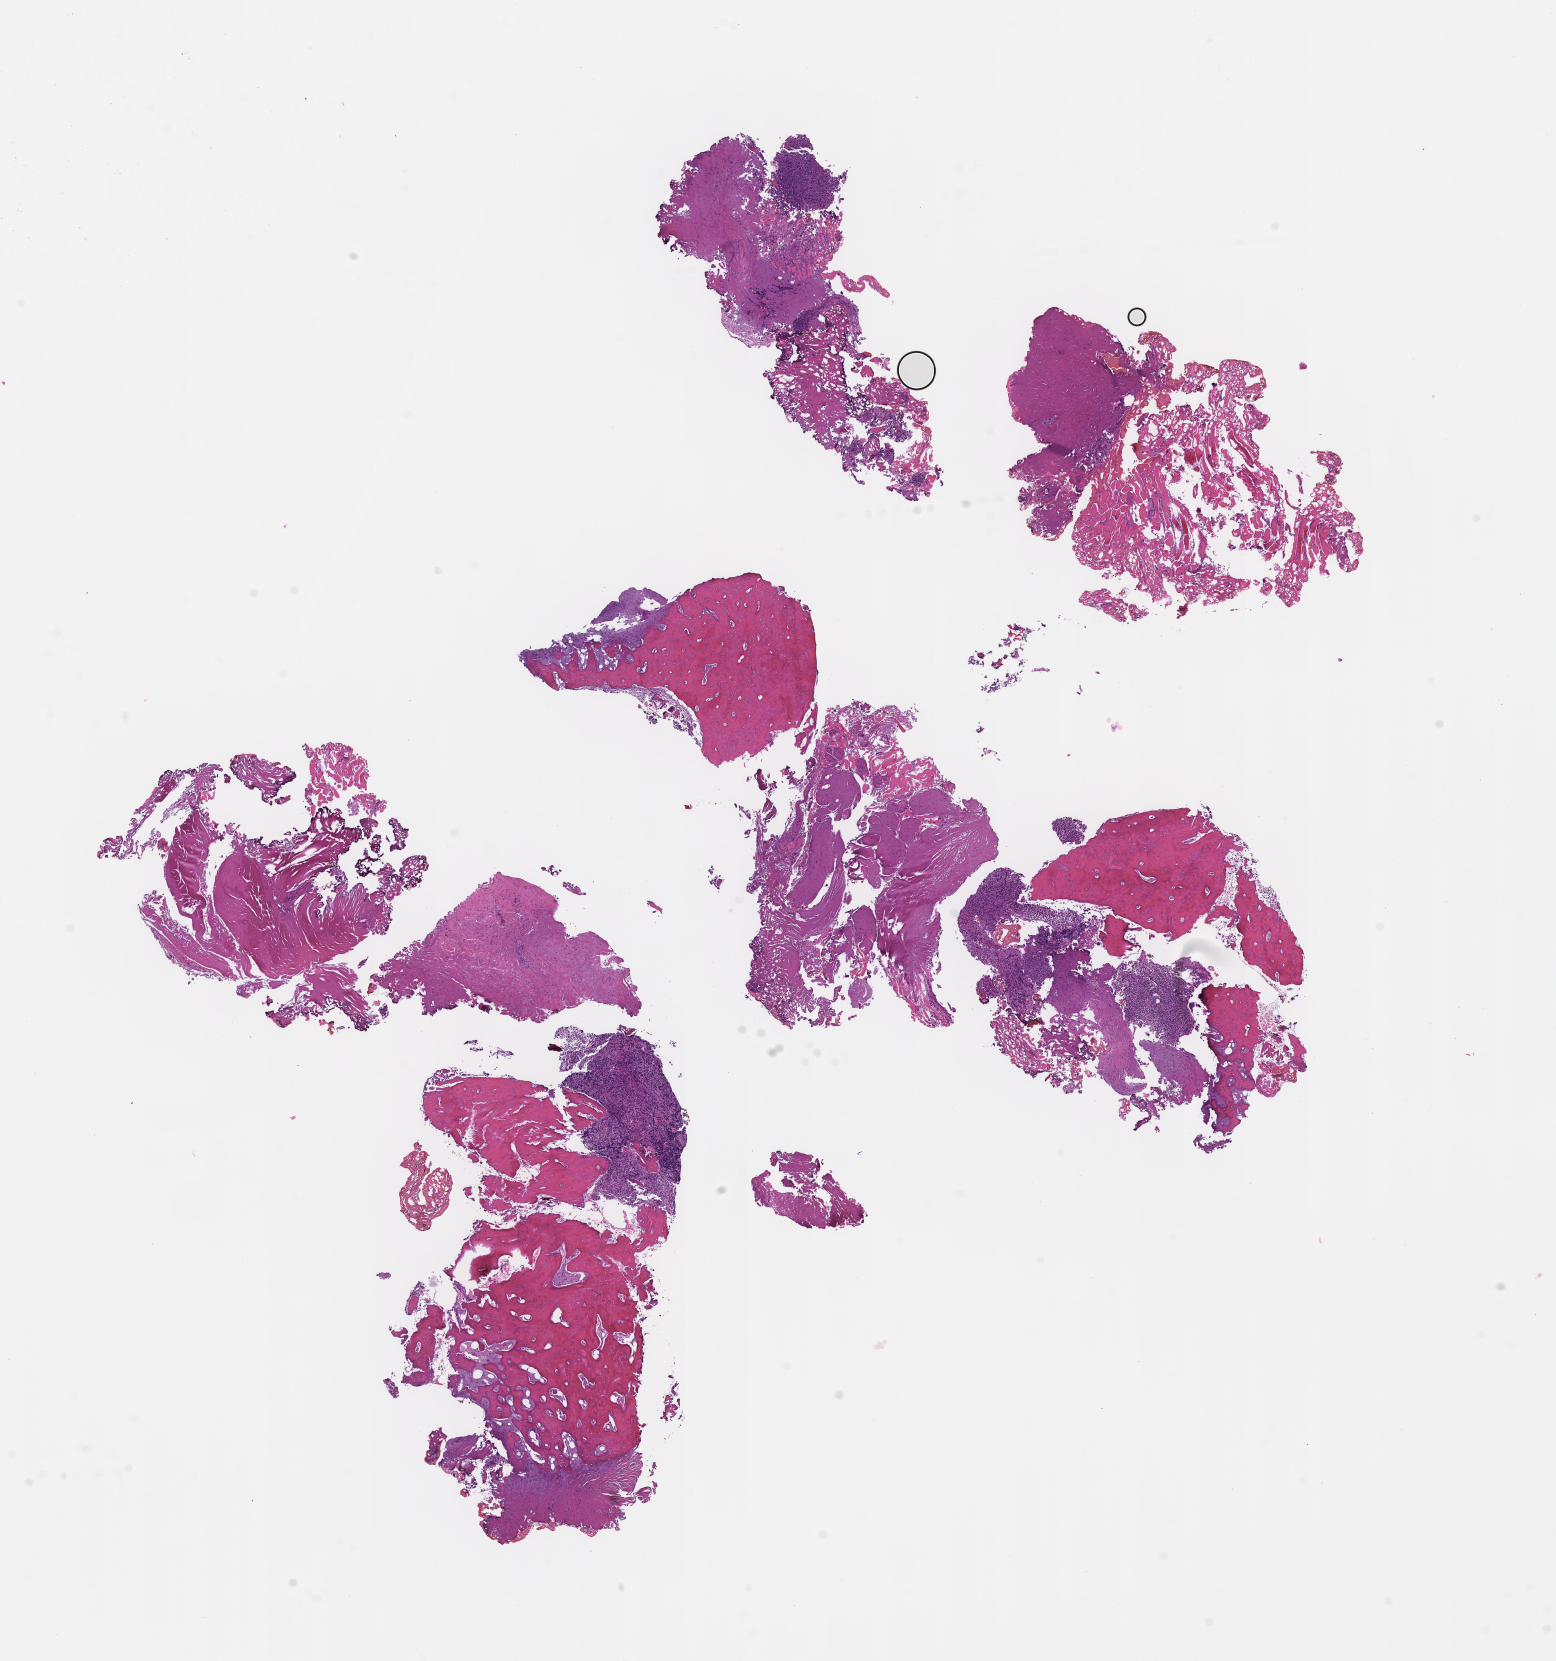
Whole-slide image, haematoxylin and eosin stain, shown as a low-resolution overview of the whole scanned area (about 12.6 x 13.4 mm); formalin-fixed, paraffin-embedded (FFPE) tissue; tissue site: bone marrow; archival tissue. Patient: female.
This section: primary tumour tissue. Diagnosis: Plasma Cell Myeloma.